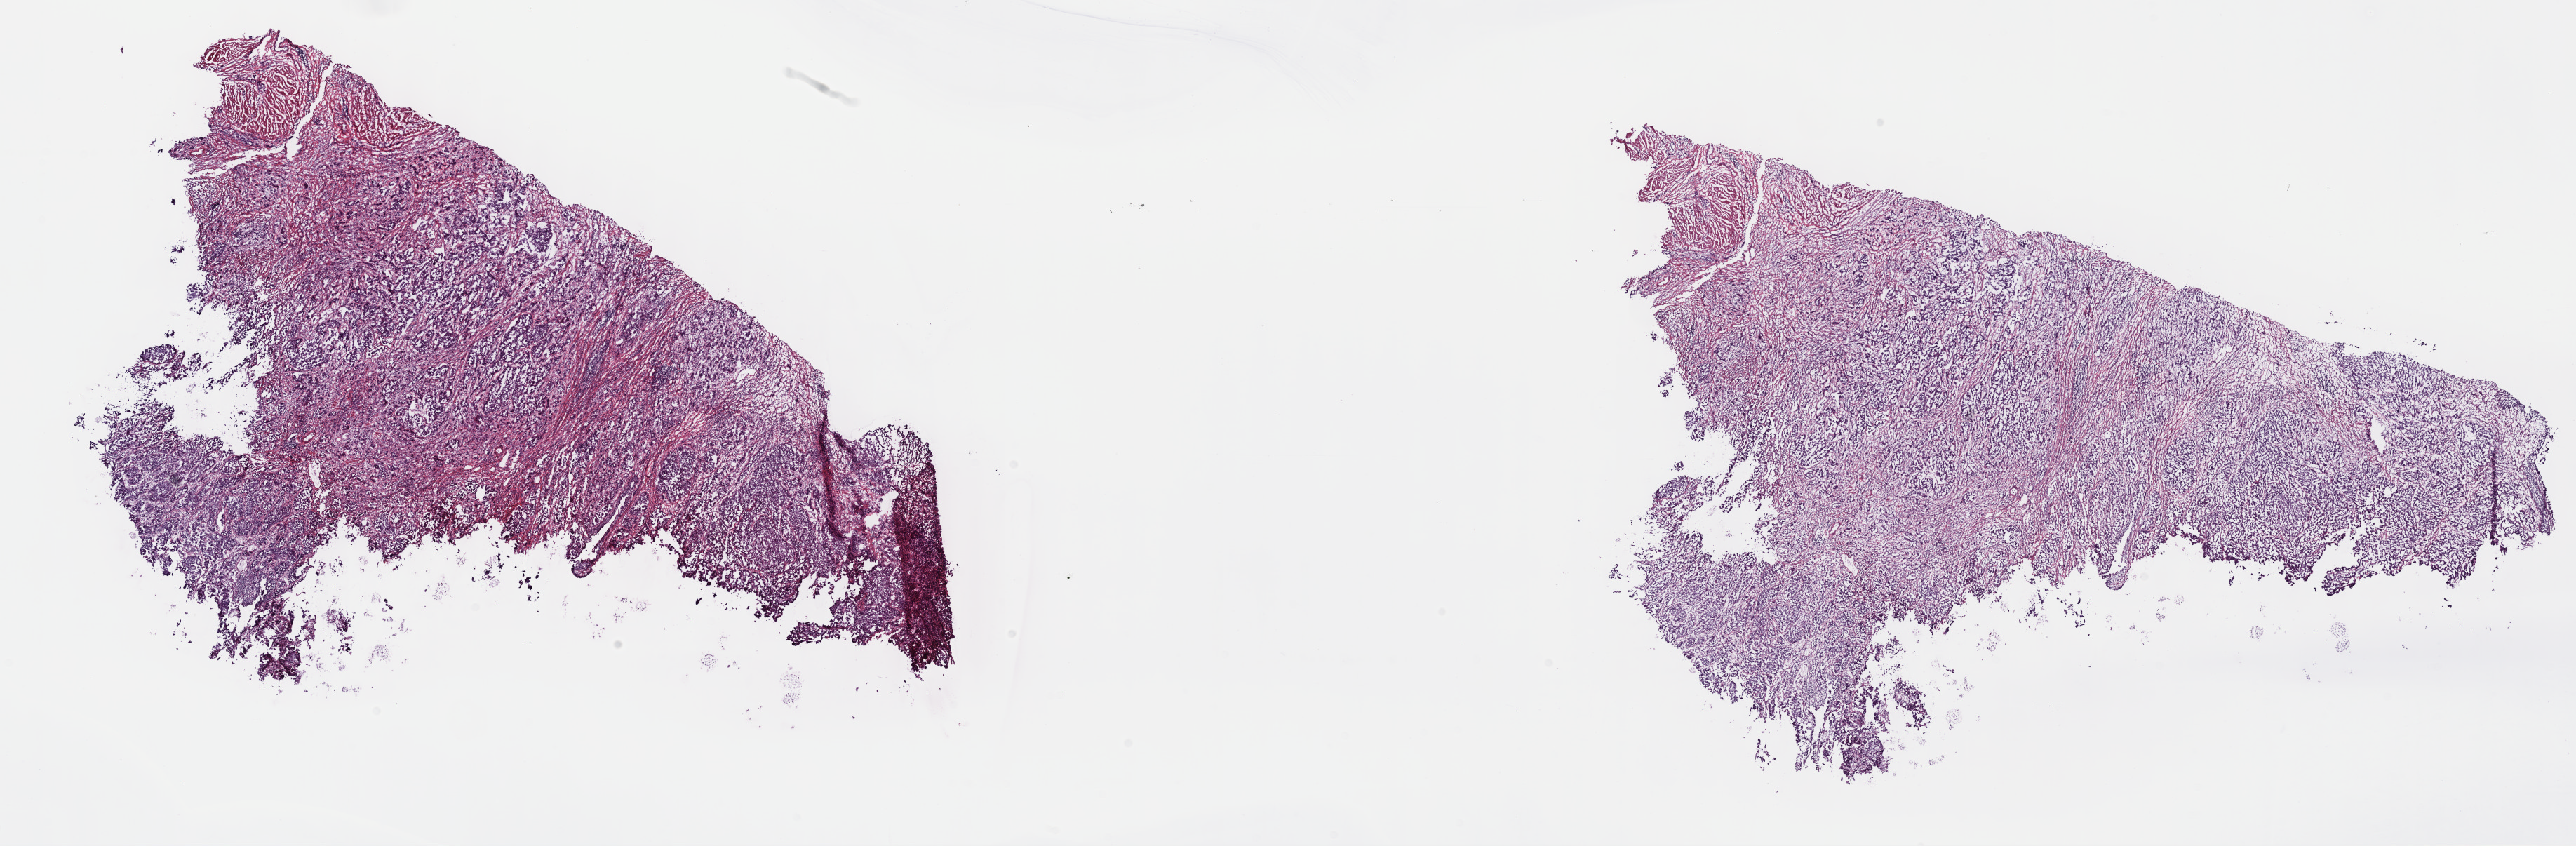
Whole-slide histology image, H&E — shown as a low-resolution overview of the whole scanned area (about 29.7 x 9.8 mm), frozen section from the top of the tissue portion, bladder, primary tumour sample. Male patient; age at initial diagnosis 77 years. Pathologist review of this section (percent, as recorded): tumour cells 75%, tumour nuclei 75%.
Diagnosis: Papillary transitional cell carcinoma.